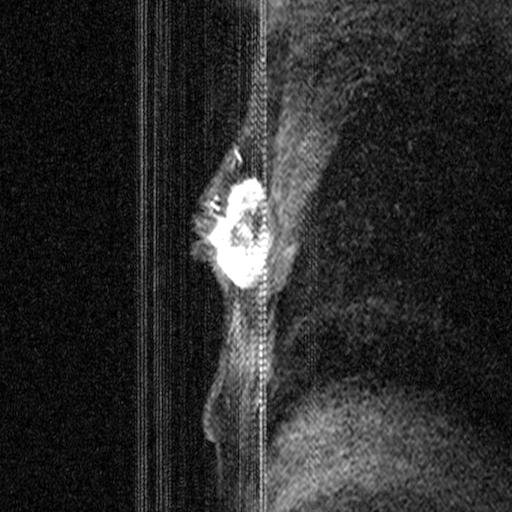
Breast MRI (dynamic contrast-enhanced), one sagittal slice; position 25 of 44 along the scan axis; dynamic contrast-enhanced study with each time point stored as its own series, time point 2 of 3 at this slice position (early post-contrast, ordered by acquisition time); 1.5 T; TE 4.5 ms, TR 11 ms; 3 mm slice thickness; 512 × 512 image matrix. Patient: female, 44 years. From the clinical record (not read from this slice): setting: breast cancer imaged before/during neoadjuvant chemotherapy; receptor status: HR-positive, HER2-negative.
Annotated regions visible in this slice (semi-automatic segmentation, software-assisted and operator-edited):
- analysis volume of interest (the breast-tissue region the enhancement analysis was run in; not a lesion): bounding box <206,164,272,299> (left, top, right, bottom; pixels)
- tumour enhancement mask (voxels above the 90 % enhancement threshold inside the analysis volume of interest): <206,164,272,297>